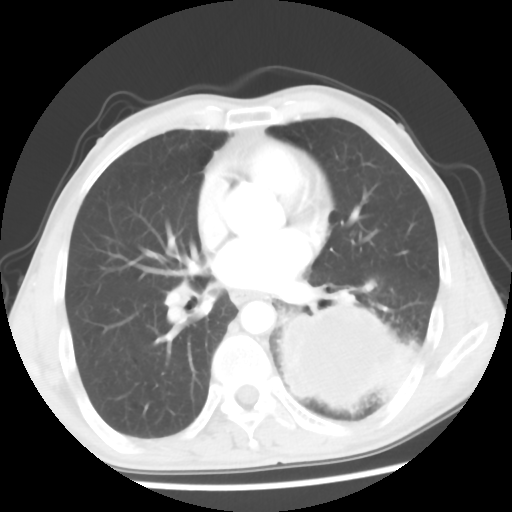
Chest CT, one axial slice. Slice 27 of 56 in the series (ordered by position). Reconstruction kernel STANDARD. 120 kVp. Lung window (W 1500 / L -600 HU). 512 × 512 image matrix, field of view 318 × 318 mm. Male patient, age 60 years. From the clinical record (not read from this slice): clinical TNM (as recorded): T4 N0 M0.
Structures marked on this image (rectangle marked by the reading radiologist):
- lung tumour (recorded histology: squamous cell carcinoma): bounding box <278,301,416,409> (left, top, right, bottom; pixels)